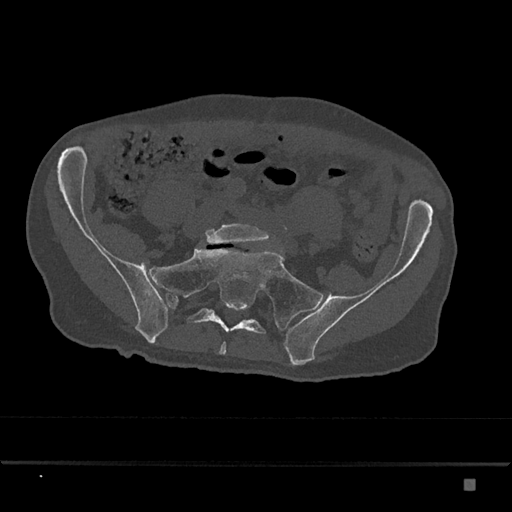
CT including the spine, one axial slice; position 218 of 797 along the scan axis; reconstruction kernel Br40s/3; 120 kVp; bone window (W 1800 / L 400 HU); 512 × 512 image matrix. Male patient, age 72 years. From the clinical record (not read from this slice): primary cancer: prostate.
Annotated regions visible in this slice (semi-automatically segmented with operator editing):
- L5 vertebra: bounding box [x1, y1, x2, y2] px = [205, 223, 269, 244]